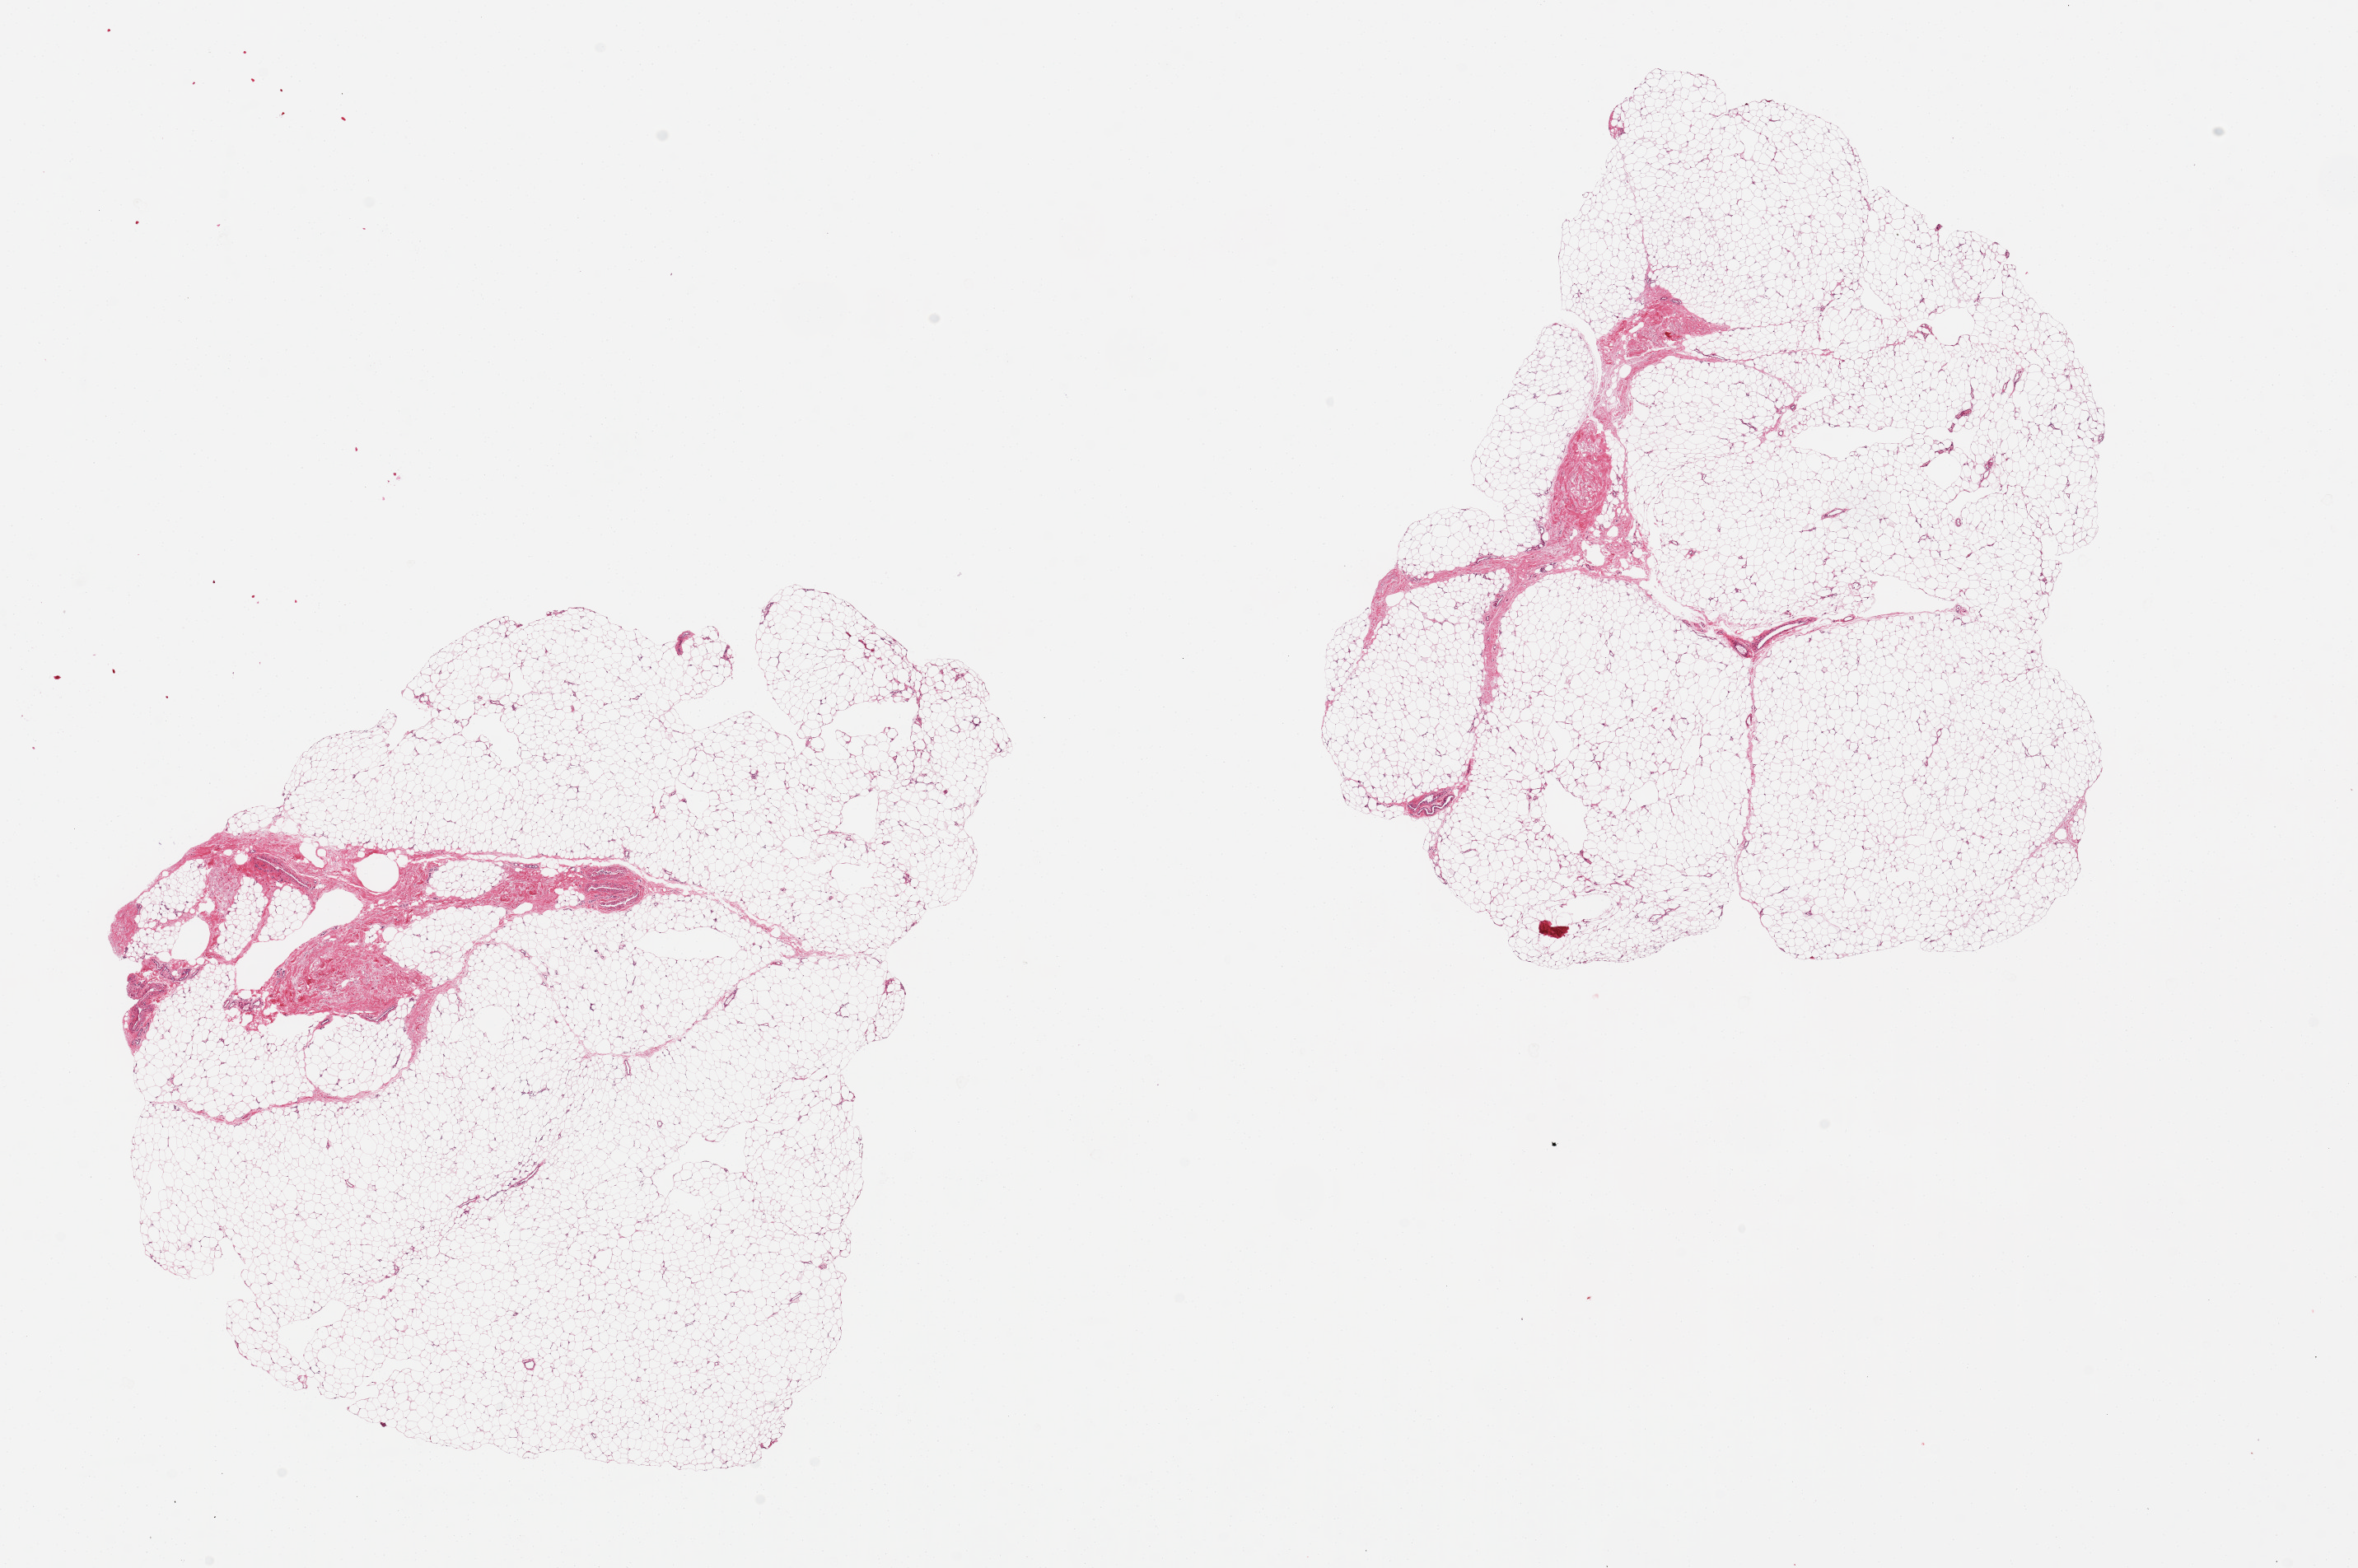
Digitized haematoxylin and eosin-stained section, brightfield — shown as a low-resolution overview of the whole scanned area (about 22.6 x 15.1 mm, acquisition: 20x scan). PAXgene-fixed paraffin-embedded (PFPE) section. Section of adipose tissue (target tissue). Donor tissue sample. Donor sex: female.
Review note (as recorded): 2 pieces, 8x7 & 8x7 mm; well fixed.